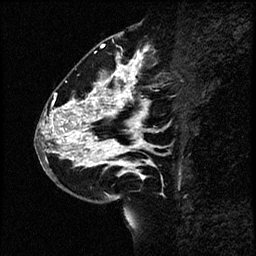
Breast MRI (dynamic contrast-enhanced), one sagittal slice. Position 30 of 60 along the scan axis. Dynamic contrast-enhanced study with each time point stored as its own series, time point 2 of 4 at this slice position (early post-contrast, ordered by acquisition time). 1.5 T. TE 4.2 ms, TR 17.6 ms. 2 mm slice thickness. 256 × 256 image matrix, field of view 200 × 200 mm. Female patient, age 43 years. Case-level facts recorded for this patient, not image findings: setting: breast cancer imaged before/during neoadjuvant chemotherapy.
Outlined on this slice (semi-automatically segmented with operator editing):
- analysis volume of interest (the breast-tissue region the enhancement analysis was run in; not a lesion): box from (x=36, y=56) to (x=169, y=191) px
- tumour enhancement mask (voxels above the 100 % enhancement threshold inside the analysis volume of interest): (x=41, y=56)–(x=156, y=177)